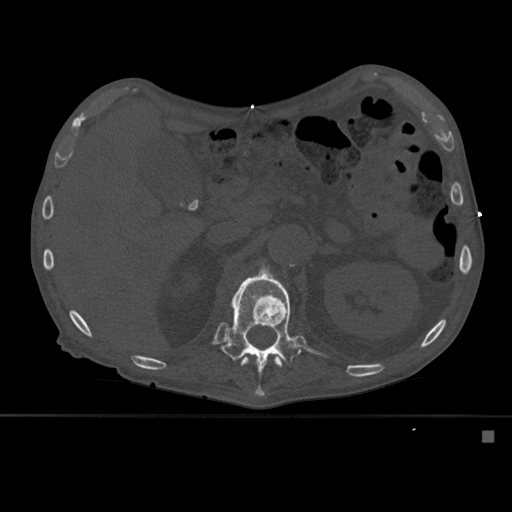
CT including the spine, one axial slice; position 260 of 527 along the scan axis; bone window (W 1800 / L 400 HU); 1.5 mm slice thickness; 512 × 512 image matrix, field of view 373 × 373 mm. Male patient, age 78 years. Case-level facts recorded for this patient, not image findings: primary cancer: prostate.
Structures marked on this image (semi-automatically segmented with operator editing):
- L1 vertebra: bounding box (x1, y1, x2, y2) in pixels: (221, 265, 301, 397)
- T12 vertebra: (241, 357, 282, 368)